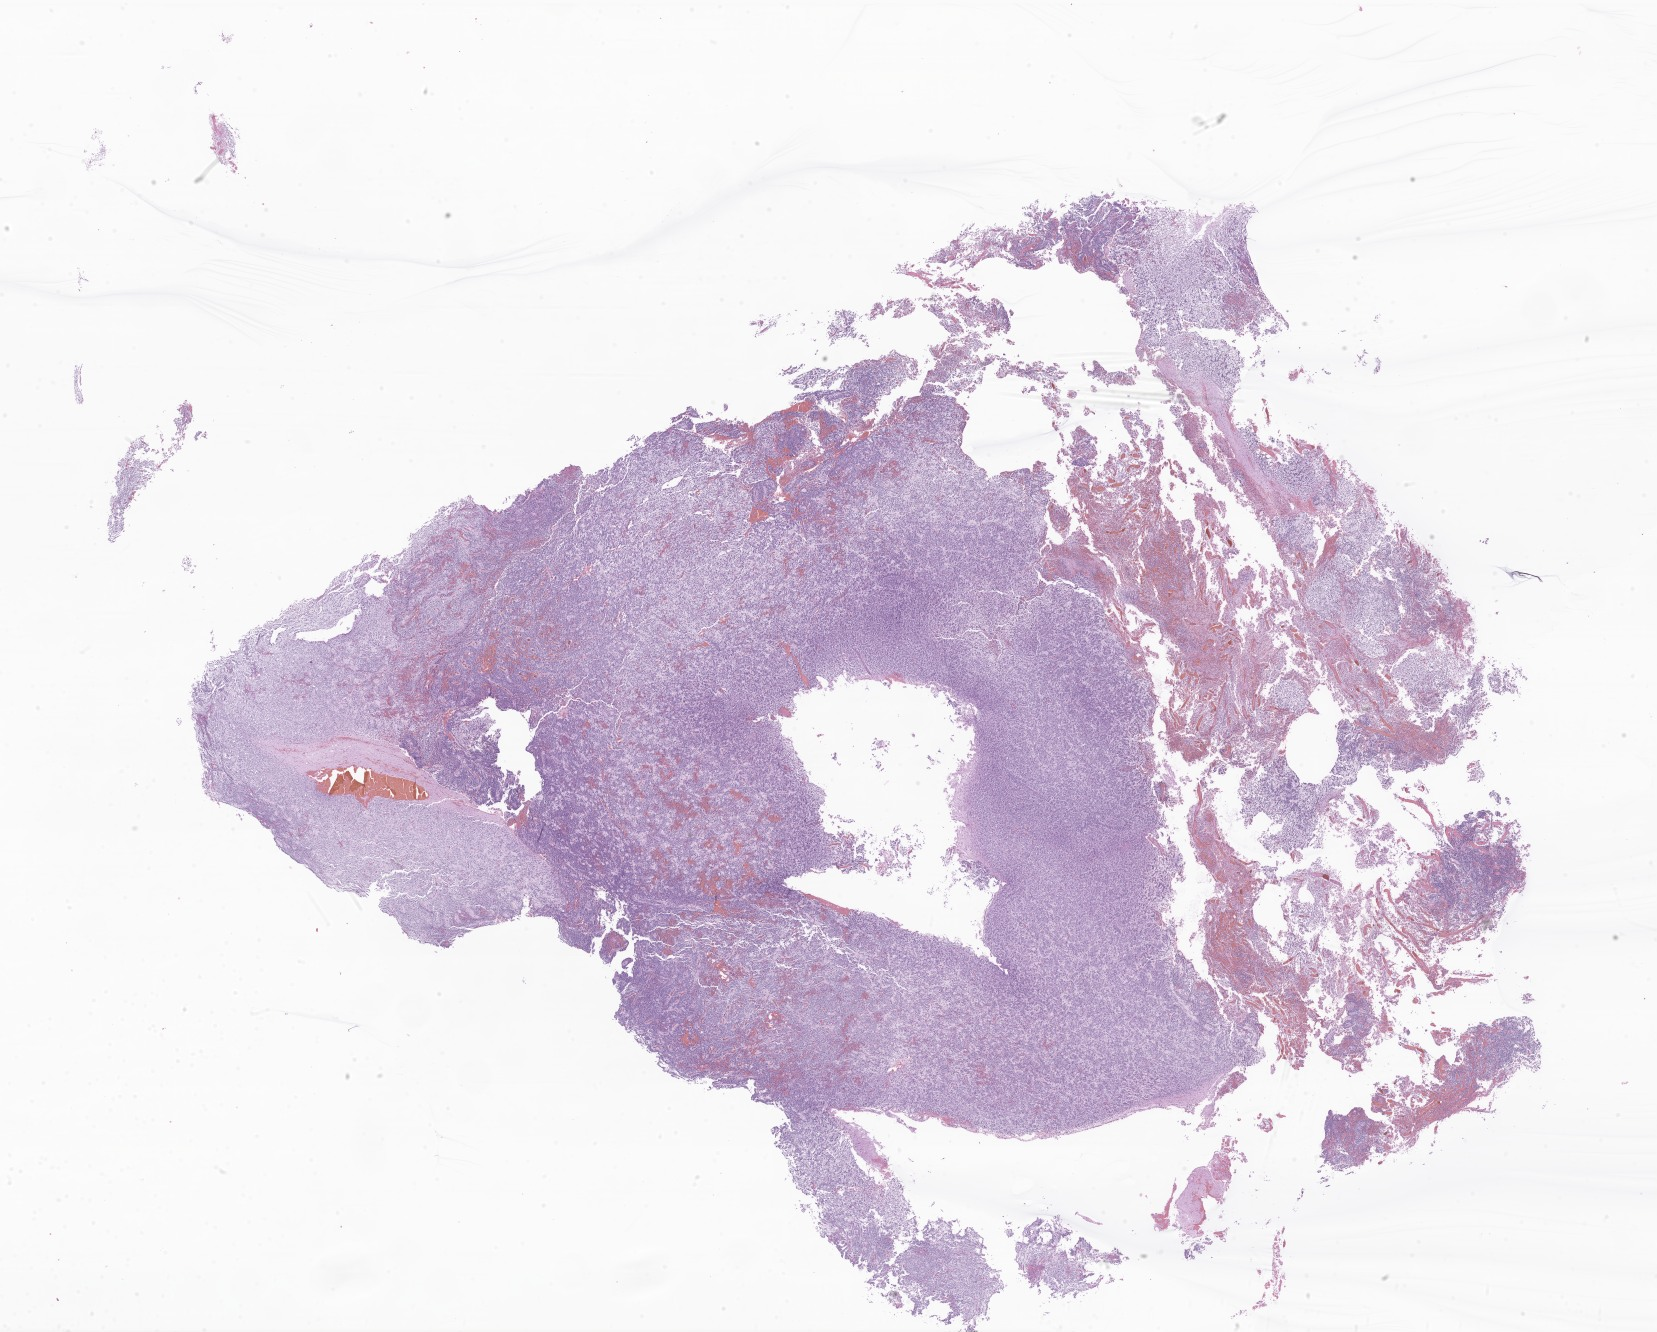
Whole-slide image, H&E stain of tumor tissue from the cerebrum, a low-resolution overview of the entire scanned area, about 27.9 x 22.5 mm, formalin-fixed paraffin-embedded section. Patient: female, age 984 days (about 2.7 years).
Recorded diagnosis: CNS embryonal tumor, NOS.